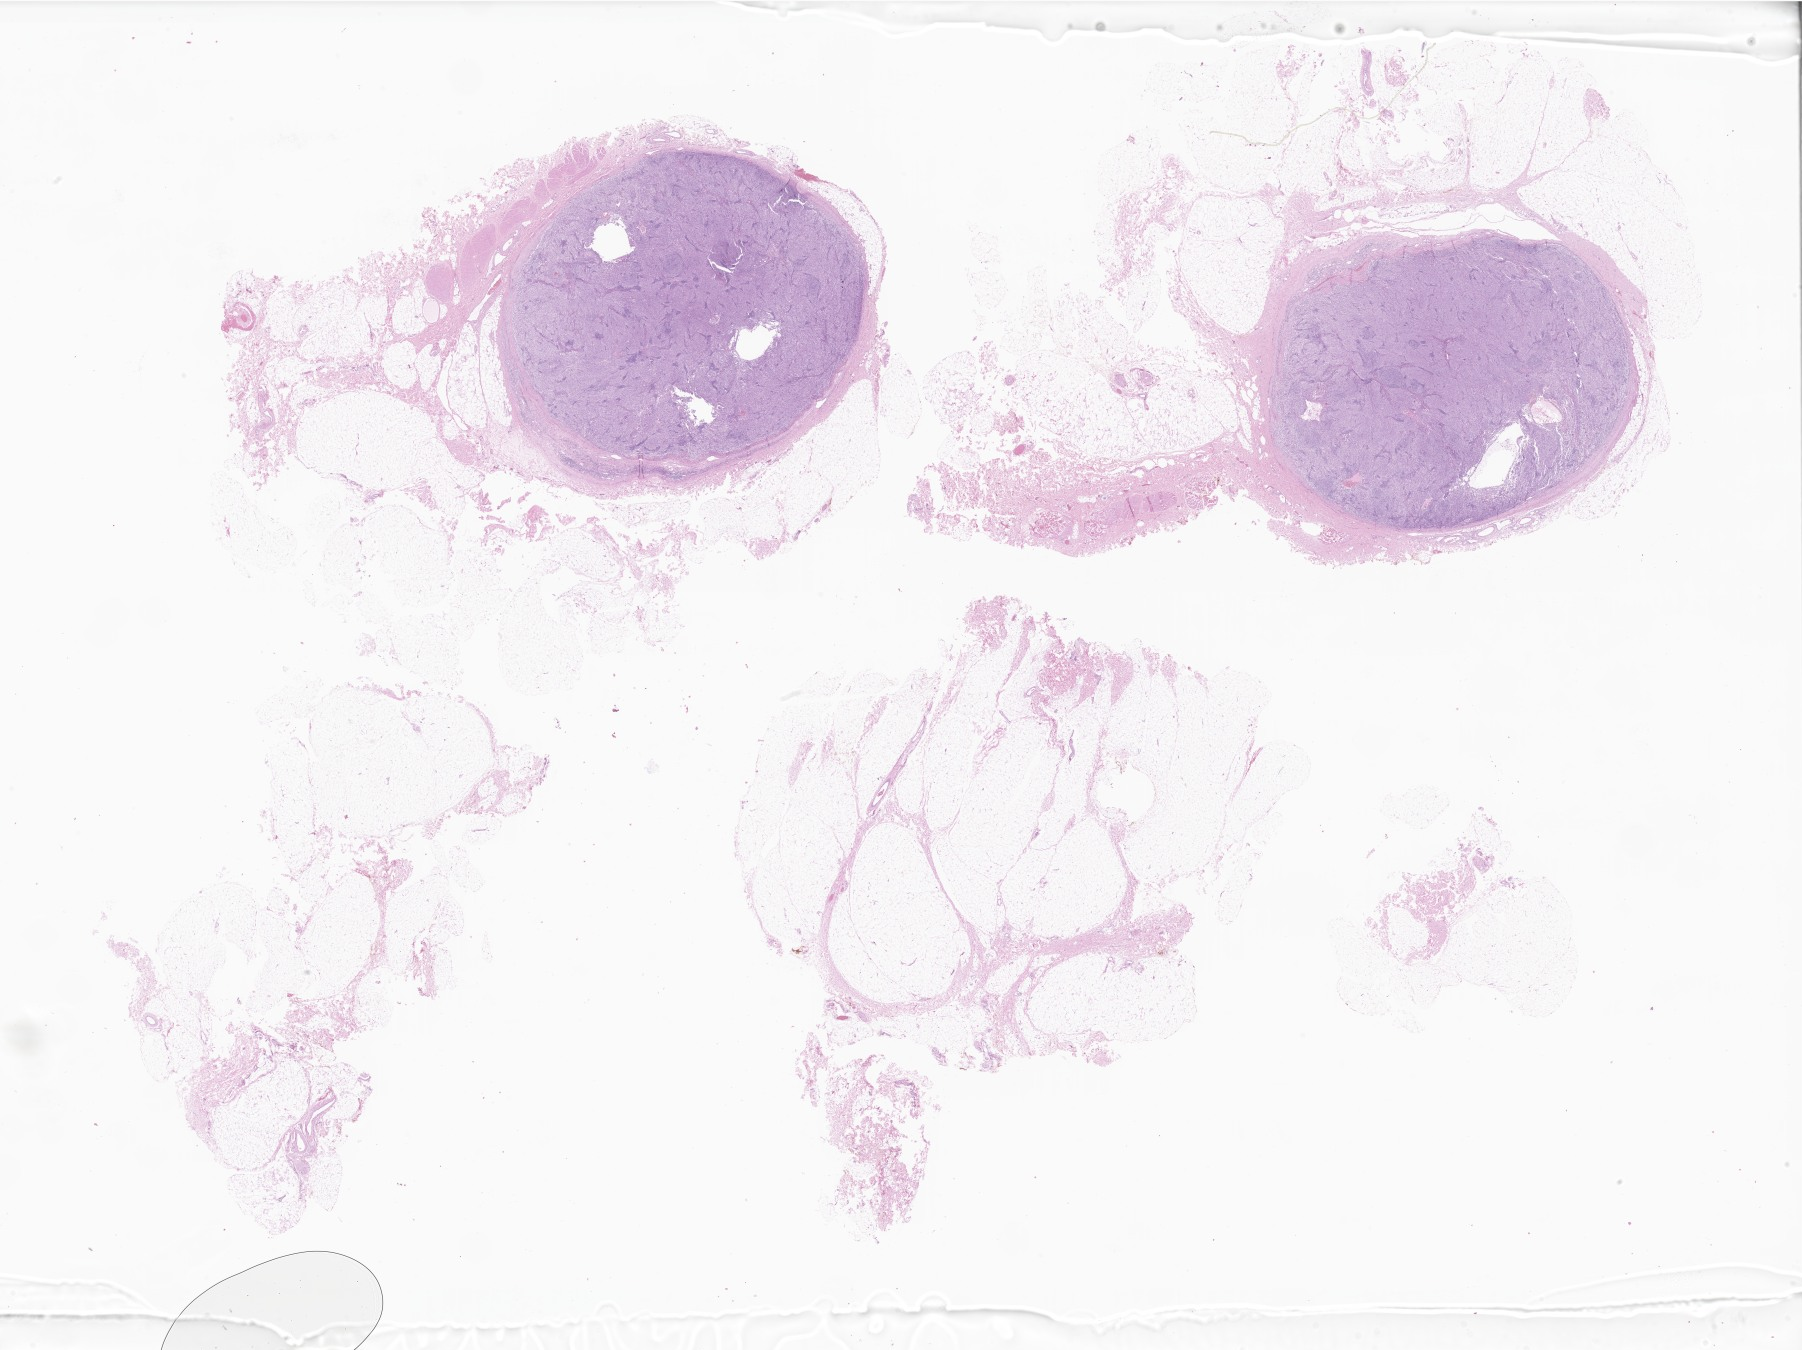
Whole-slide image, H&E stain of tumor tissue from the soft tissues of head and neck, shown as a low-resolution overview of the whole scanned area (about 30.4 x 22.8 mm), formalin-fixed, paraffin-embedded (FFPE) tissue. Patient: male, age 147 days.
Tissue or organ of origin (case record): connective, subcutaneous and other soft tissues of head, face, and neck. Diagnosis: Epithelial-myoepithelial carcinoma.